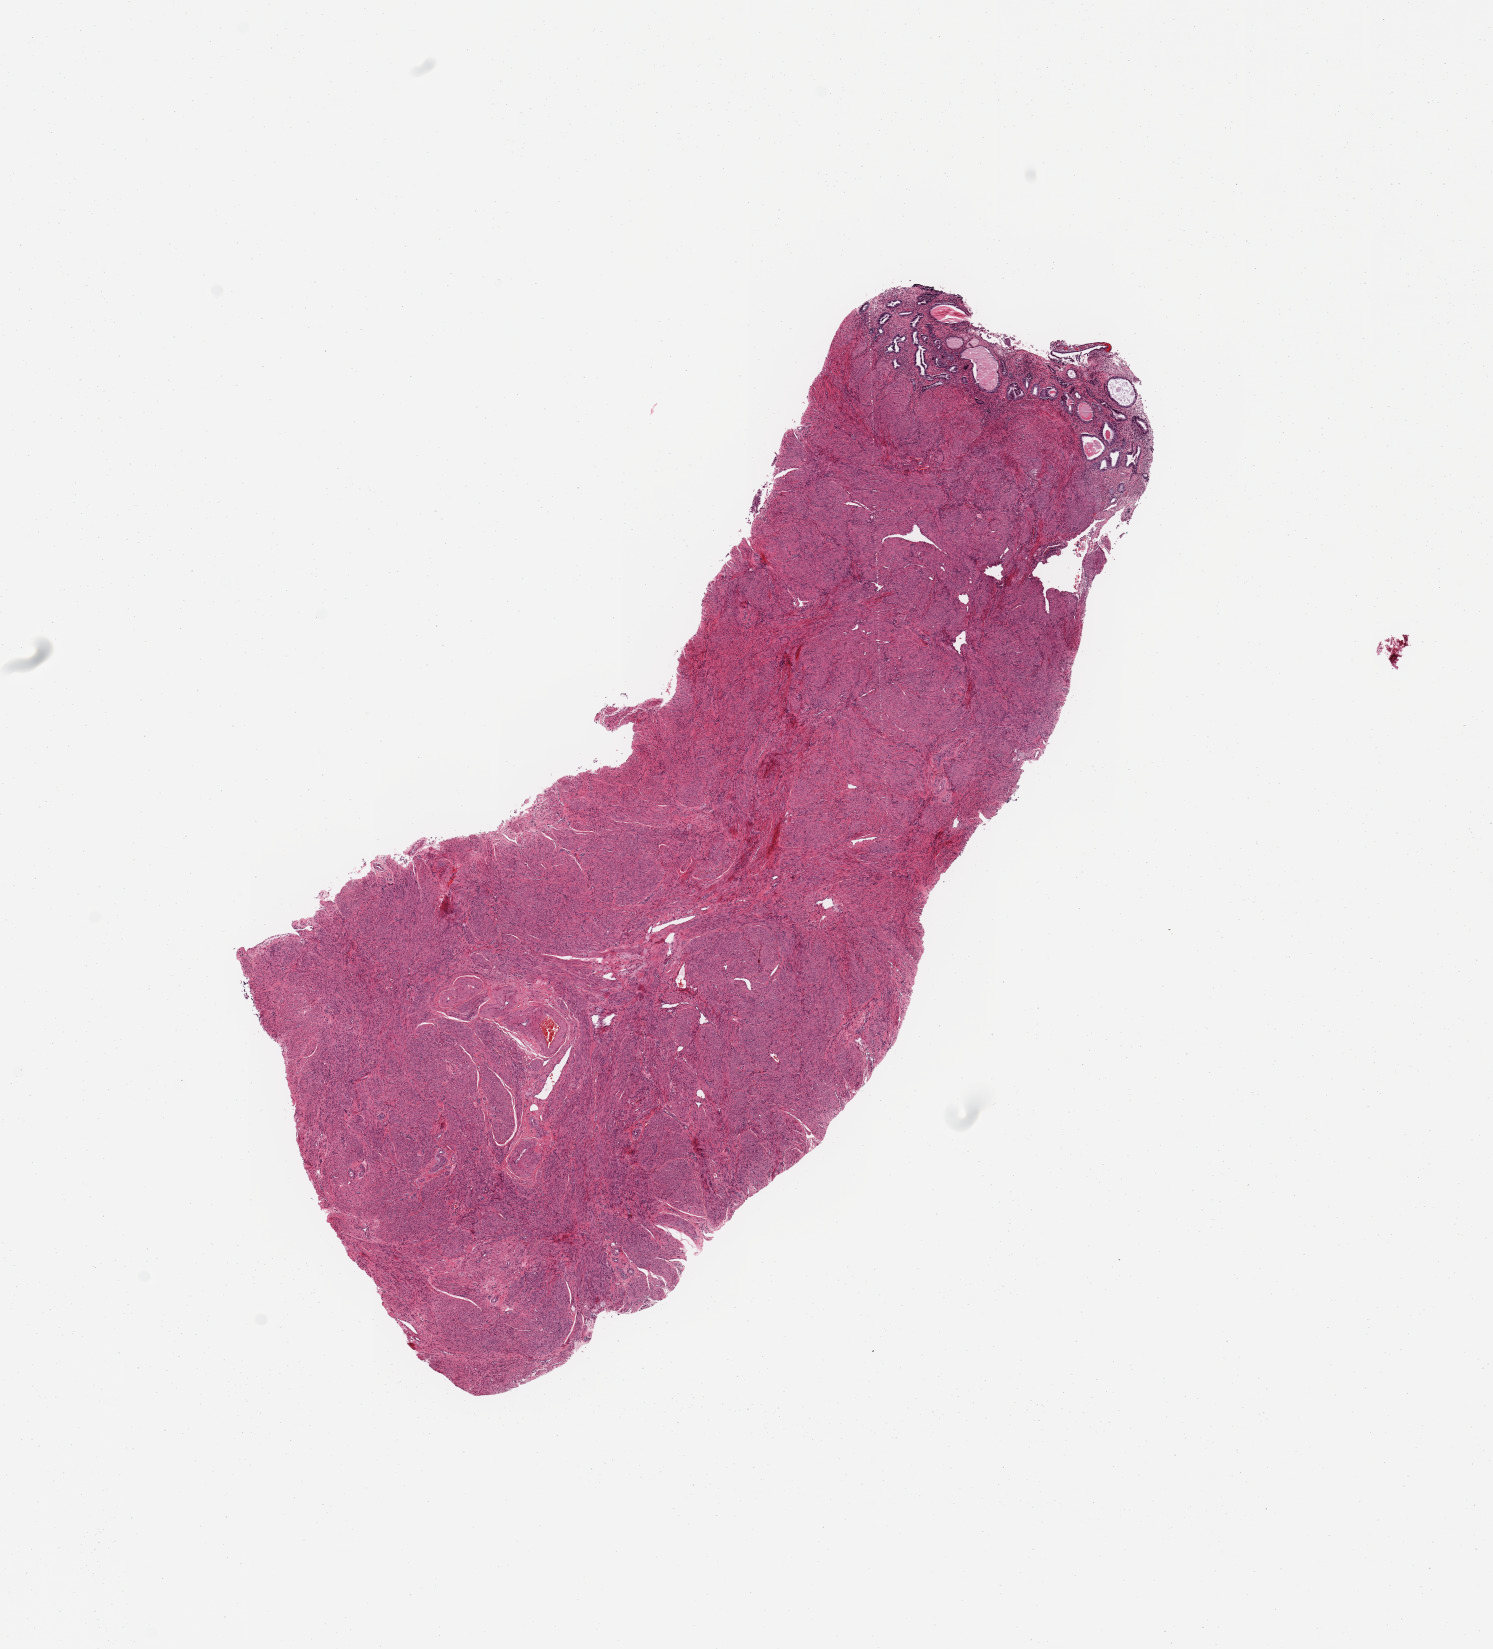
Digitized H&E tissue section (whole slide) — a low-resolution overview of the entire scanned area, about 11.8 x 13.0 mm (from a 20x scan). Normal (non-tumour) tissue sample, sampled site: uterus. 68-year-old female patient.
* this section: normal (non-tumour) tissue from the same patient
* patient diagnosis: Endometrioid adenocarcinoma, NOS